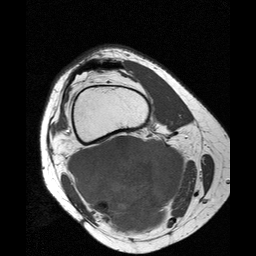
MRI of an extremity soft-tissue mass, one axial slice; position 18 of 25 along the scan axis; 256 × 256 image matrix, field of view 160 × 160 mm. Female patient. From the clinical record (not read from this slice): histological type: liposarcoma; site of the primary tumour: right thigh.
Annotated regions visible in this slice (expert manual segmentation):
- gross tumour volume (mass): bounding box (x1, y1, x2, y2) in pixels: (68, 135, 187, 236)